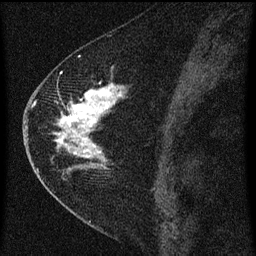
Breast MRI (dynamic contrast-enhanced), one sagittal slice. Slice 31 of 60 in the series (ordered by position). Dynamic contrast-enhanced series, image 2 of 3 at this slice position (ordered by acquisition). 1.5 T. TE 4.2 ms, TR 8 ms. 2 mm slice thickness. 256 × 256 image matrix, field of view 180 × 180 mm. Patient: female, 47 years.
Outlined on this slice (semi-automatically segmented with operator editing):
- analysis volume of interest (the breast-tissue region the enhancement analysis was run in; not a lesion): bounding box [x1, y1, x2, y2] px = [38, 76, 129, 193]
- tumour enhancement mask (voxels above the 70 % enhancement threshold inside the analysis volume of interest): [55, 84, 125, 171]